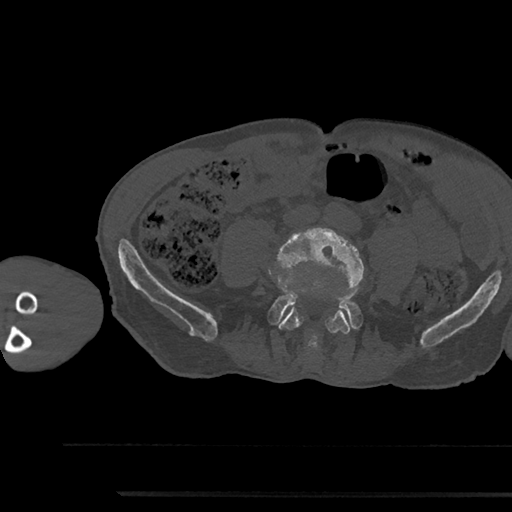
CT including the spine, one axial slice. Position 381 of 797 along the scan axis. Reconstruction kernel Br40s/3. Bone window (W 1800 / L 400 HU). 0.5 mm slice thickness. 512 × 512 image matrix, field of view 367 × 367 mm. Patient: male, 79 years. Case-level facts recorded for this patient, not image findings: primary cancer: prostate.
Annotated regions visible in this slice (semi-automatic segmentation, software-assisted and operator-edited):
- L4 vertebra: box from (x=272, y=227) to (x=364, y=350) px
- L5 vertebra: (x=270, y=293)–(x=362, y=330)